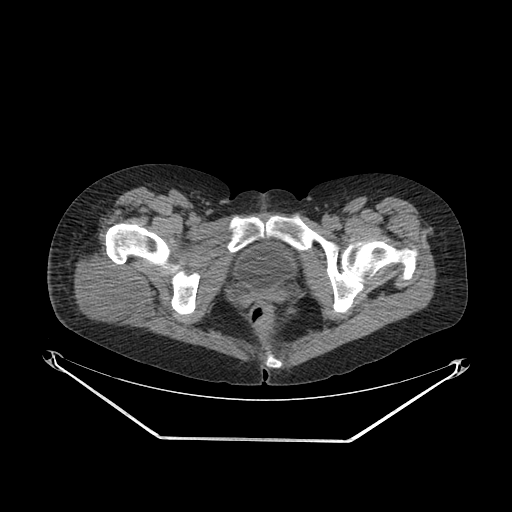
CT of an extremity soft-tissue mass (from a PET/CT study), one axial slice. Slice 44 of 267 in the series (ordered by position). 140 kVp. Soft-tissue window (W 400 / L 40 HU). 512 × 512 image matrix, field of view 500 × 500 mm. Female patient. Case-level facts recorded for this patient, not image findings: histological type: epithelioid sarcoma with vascular differentiation; site of the primary tumour: right buttock.
Structures marked on this image (expert contour drawn on MRI and transferred to this co-registered scan by the dataset authors):
- gross tumour volume (mass): bounding box (x1, y1, x2, y2) in pixels: (66, 247, 156, 332)